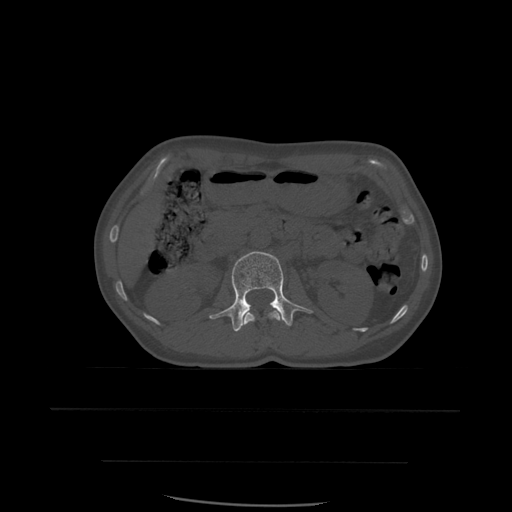
CT including the spine, one axial slice. Slice 231 of 574 in the series (ordered by position). Bone window (W 1800 / L 400 HU). 512 × 512 image matrix, field of view 392 × 392 mm. Patient age 48 years. From the clinical record (not read from this slice): primary cancer: lung.
Structures marked on this image (semi-automatic segmentation, software-assisted and operator-edited):
- L1 vertebra: bounding box <244,310,282,339> (left, top, right, bottom; pixels)
- L2 vertebra: <209,252,313,332>